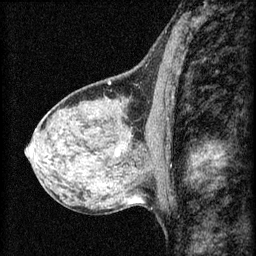
Breast MRI (dynamic contrast-enhanced), one sagittal slice. Position 34 of 60 along the scan axis. 3 images stored at this slice position (order not interpretable as contrast timing). 1.5 T. TE 4.2 ms, TR 8.2 ms. 2 mm slice thickness. 256 × 256 image matrix, field of view 180 × 180 mm. Patient: female, 40 years.
Structures marked on this image (semi-automatic segmentation, software-assisted and operator-edited):
- analysis volume of interest (the breast-tissue region the enhancement analysis was run in; not a lesion): bounding box [x1, y1, x2, y2] px = [104, 116, 141, 165]
- tumour enhancement mask (voxels above the 70 % enhancement threshold inside the analysis volume of interest): [116, 152, 119, 155]